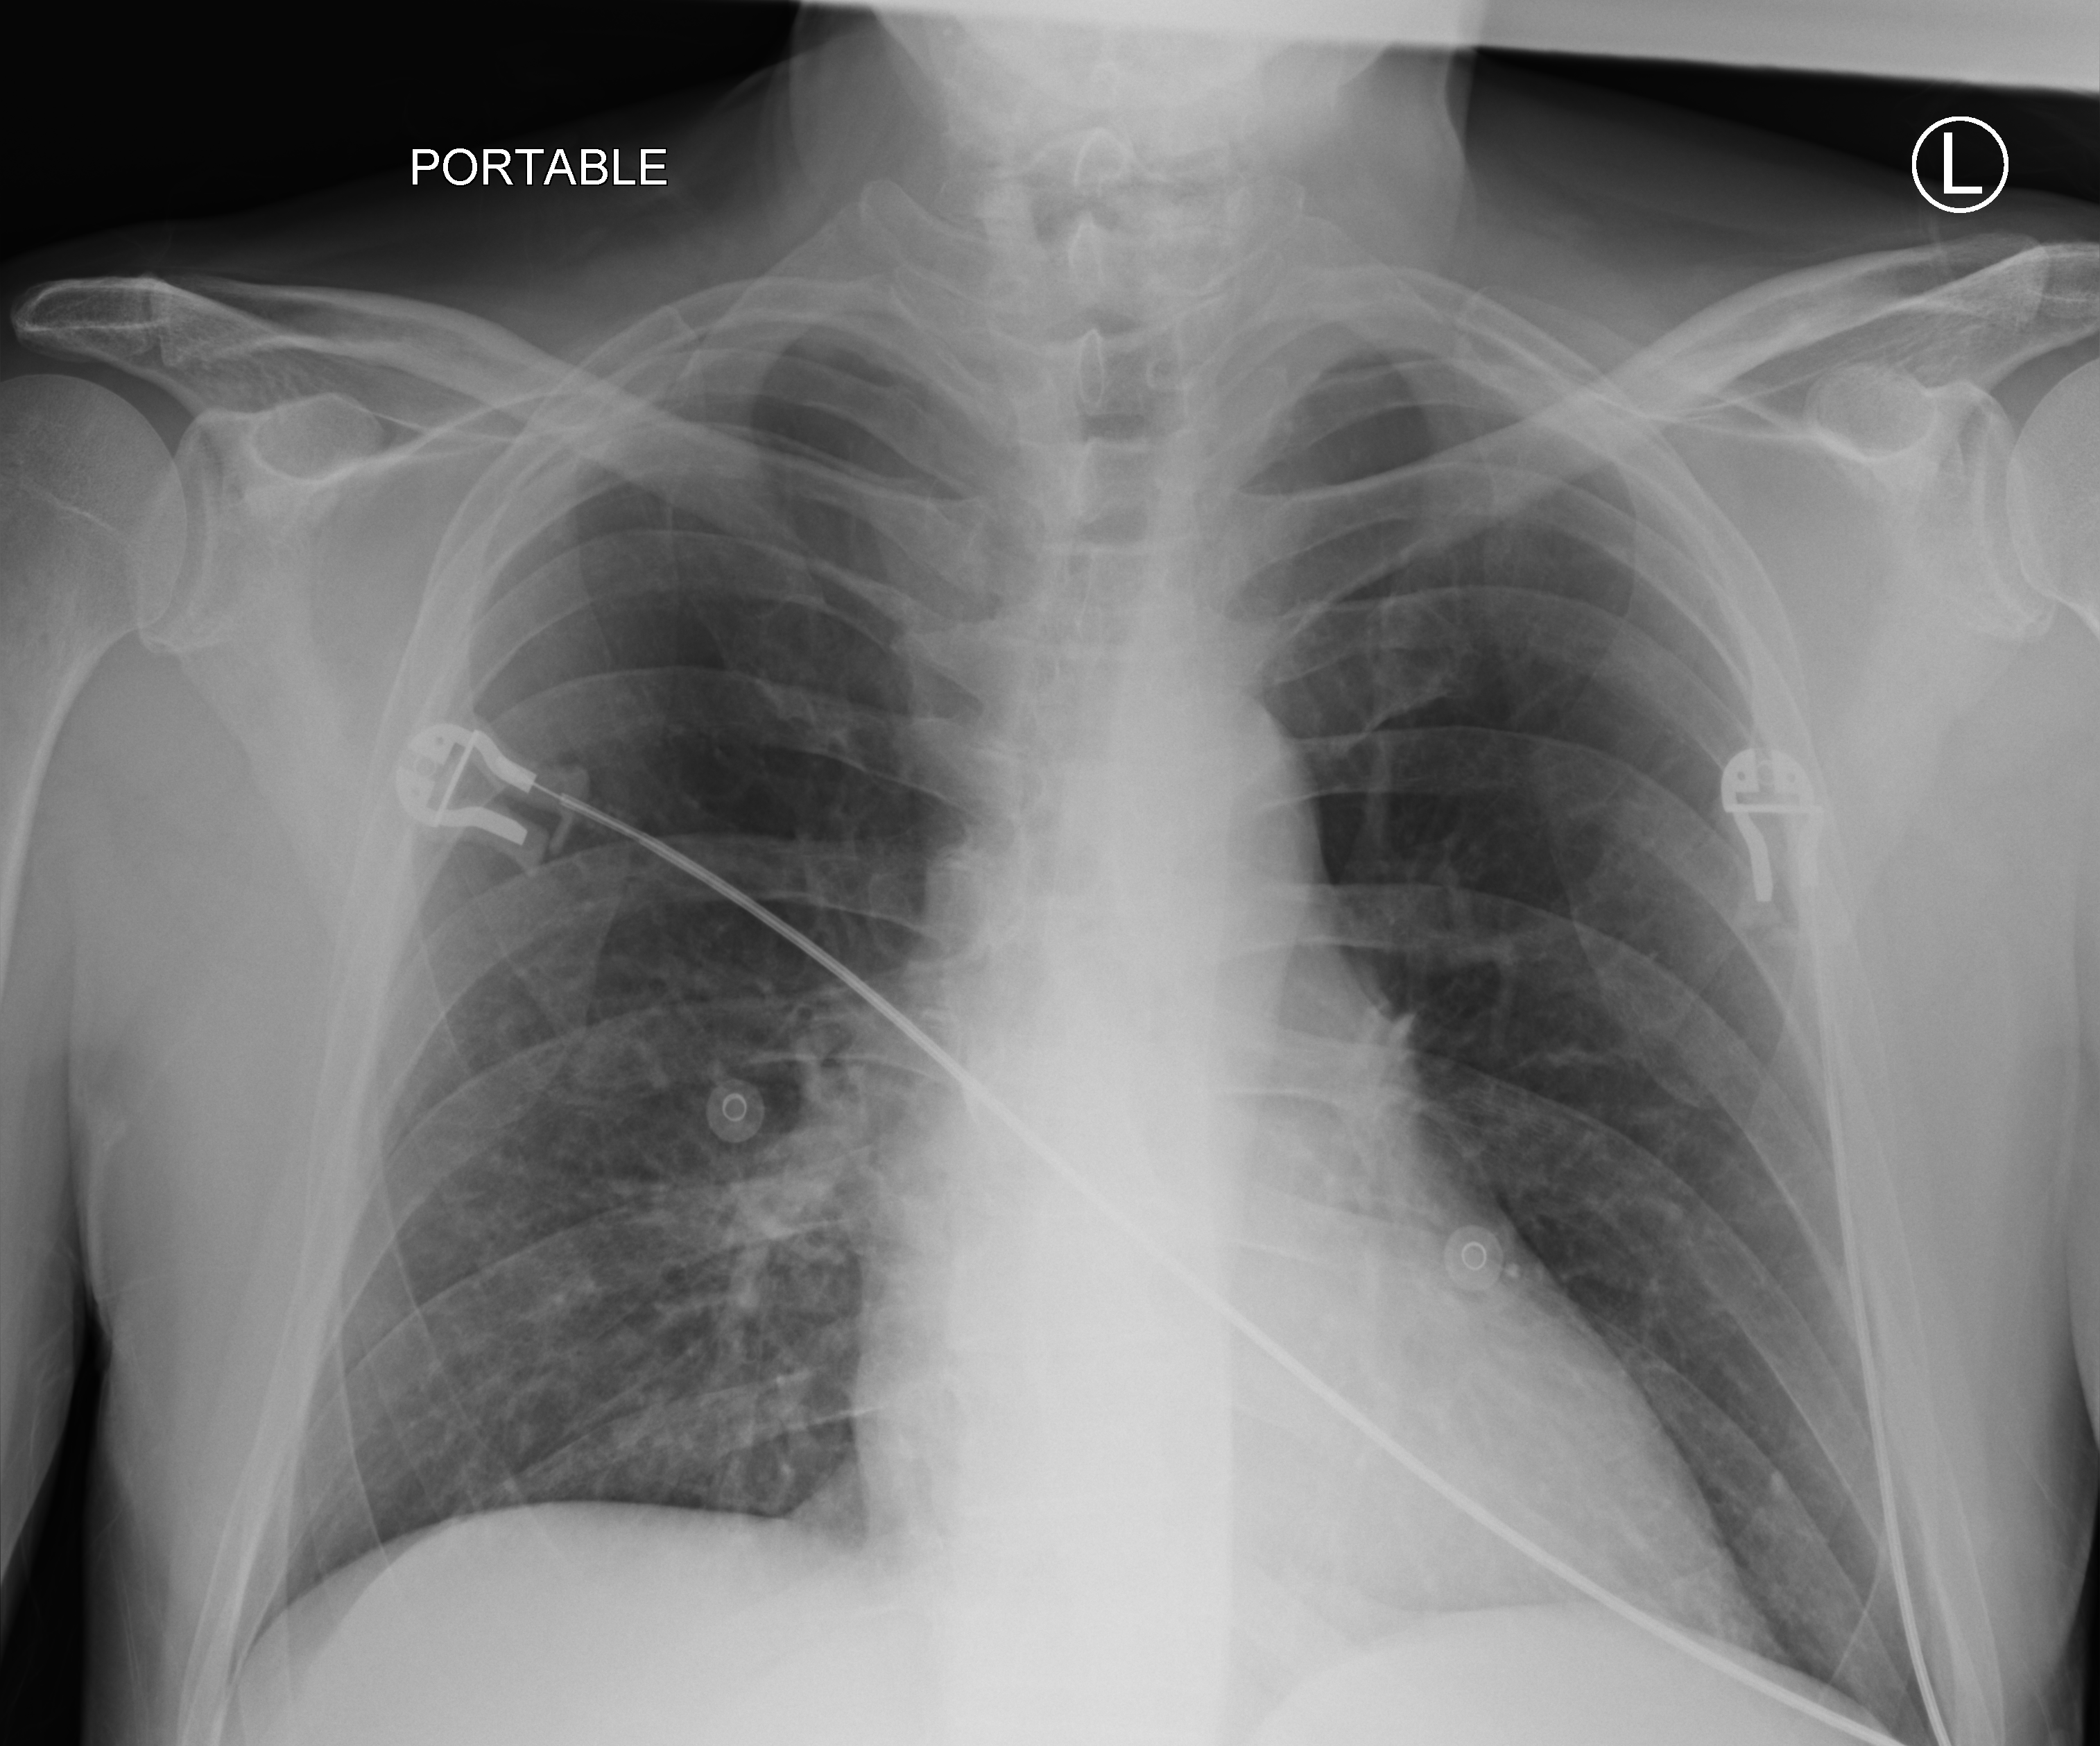
Portable chest radiograph; anteroposterior (AP) projection. Male patient hospitalised with COVID-19, age 60–74 years.
Admission-level facts for this patient (not findings on this image; timing relative to this image not recorded): length of hospital stay: 4 days; mechanically ventilated during this hospital stay: no; admitted to intensive care during this hospital stay: no.